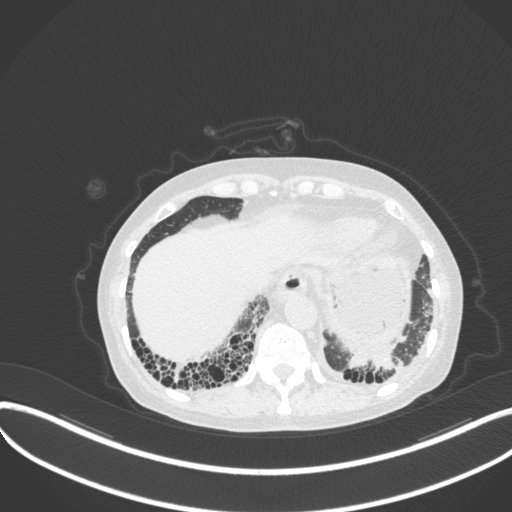
Chest CT, one axial slice. Position 55 of 373 along the scan axis. 120 kVp. Lung window (W 1500 / L -600 HU). 1 mm slice thickness. 512 × 512 image matrix, field of view 400 × 400 mm. Patient: female, 56 years. Case-level facts recorded for this patient, not image findings: clinical TNM (as recorded): T1 N0 M0.
Annotated regions visible in this slice (rectangle marked by the reading radiologist):
- lung tumour (recorded histology: adenocarcinoma): bounding box <340,346,404,378> (left, top, right, bottom; pixels)